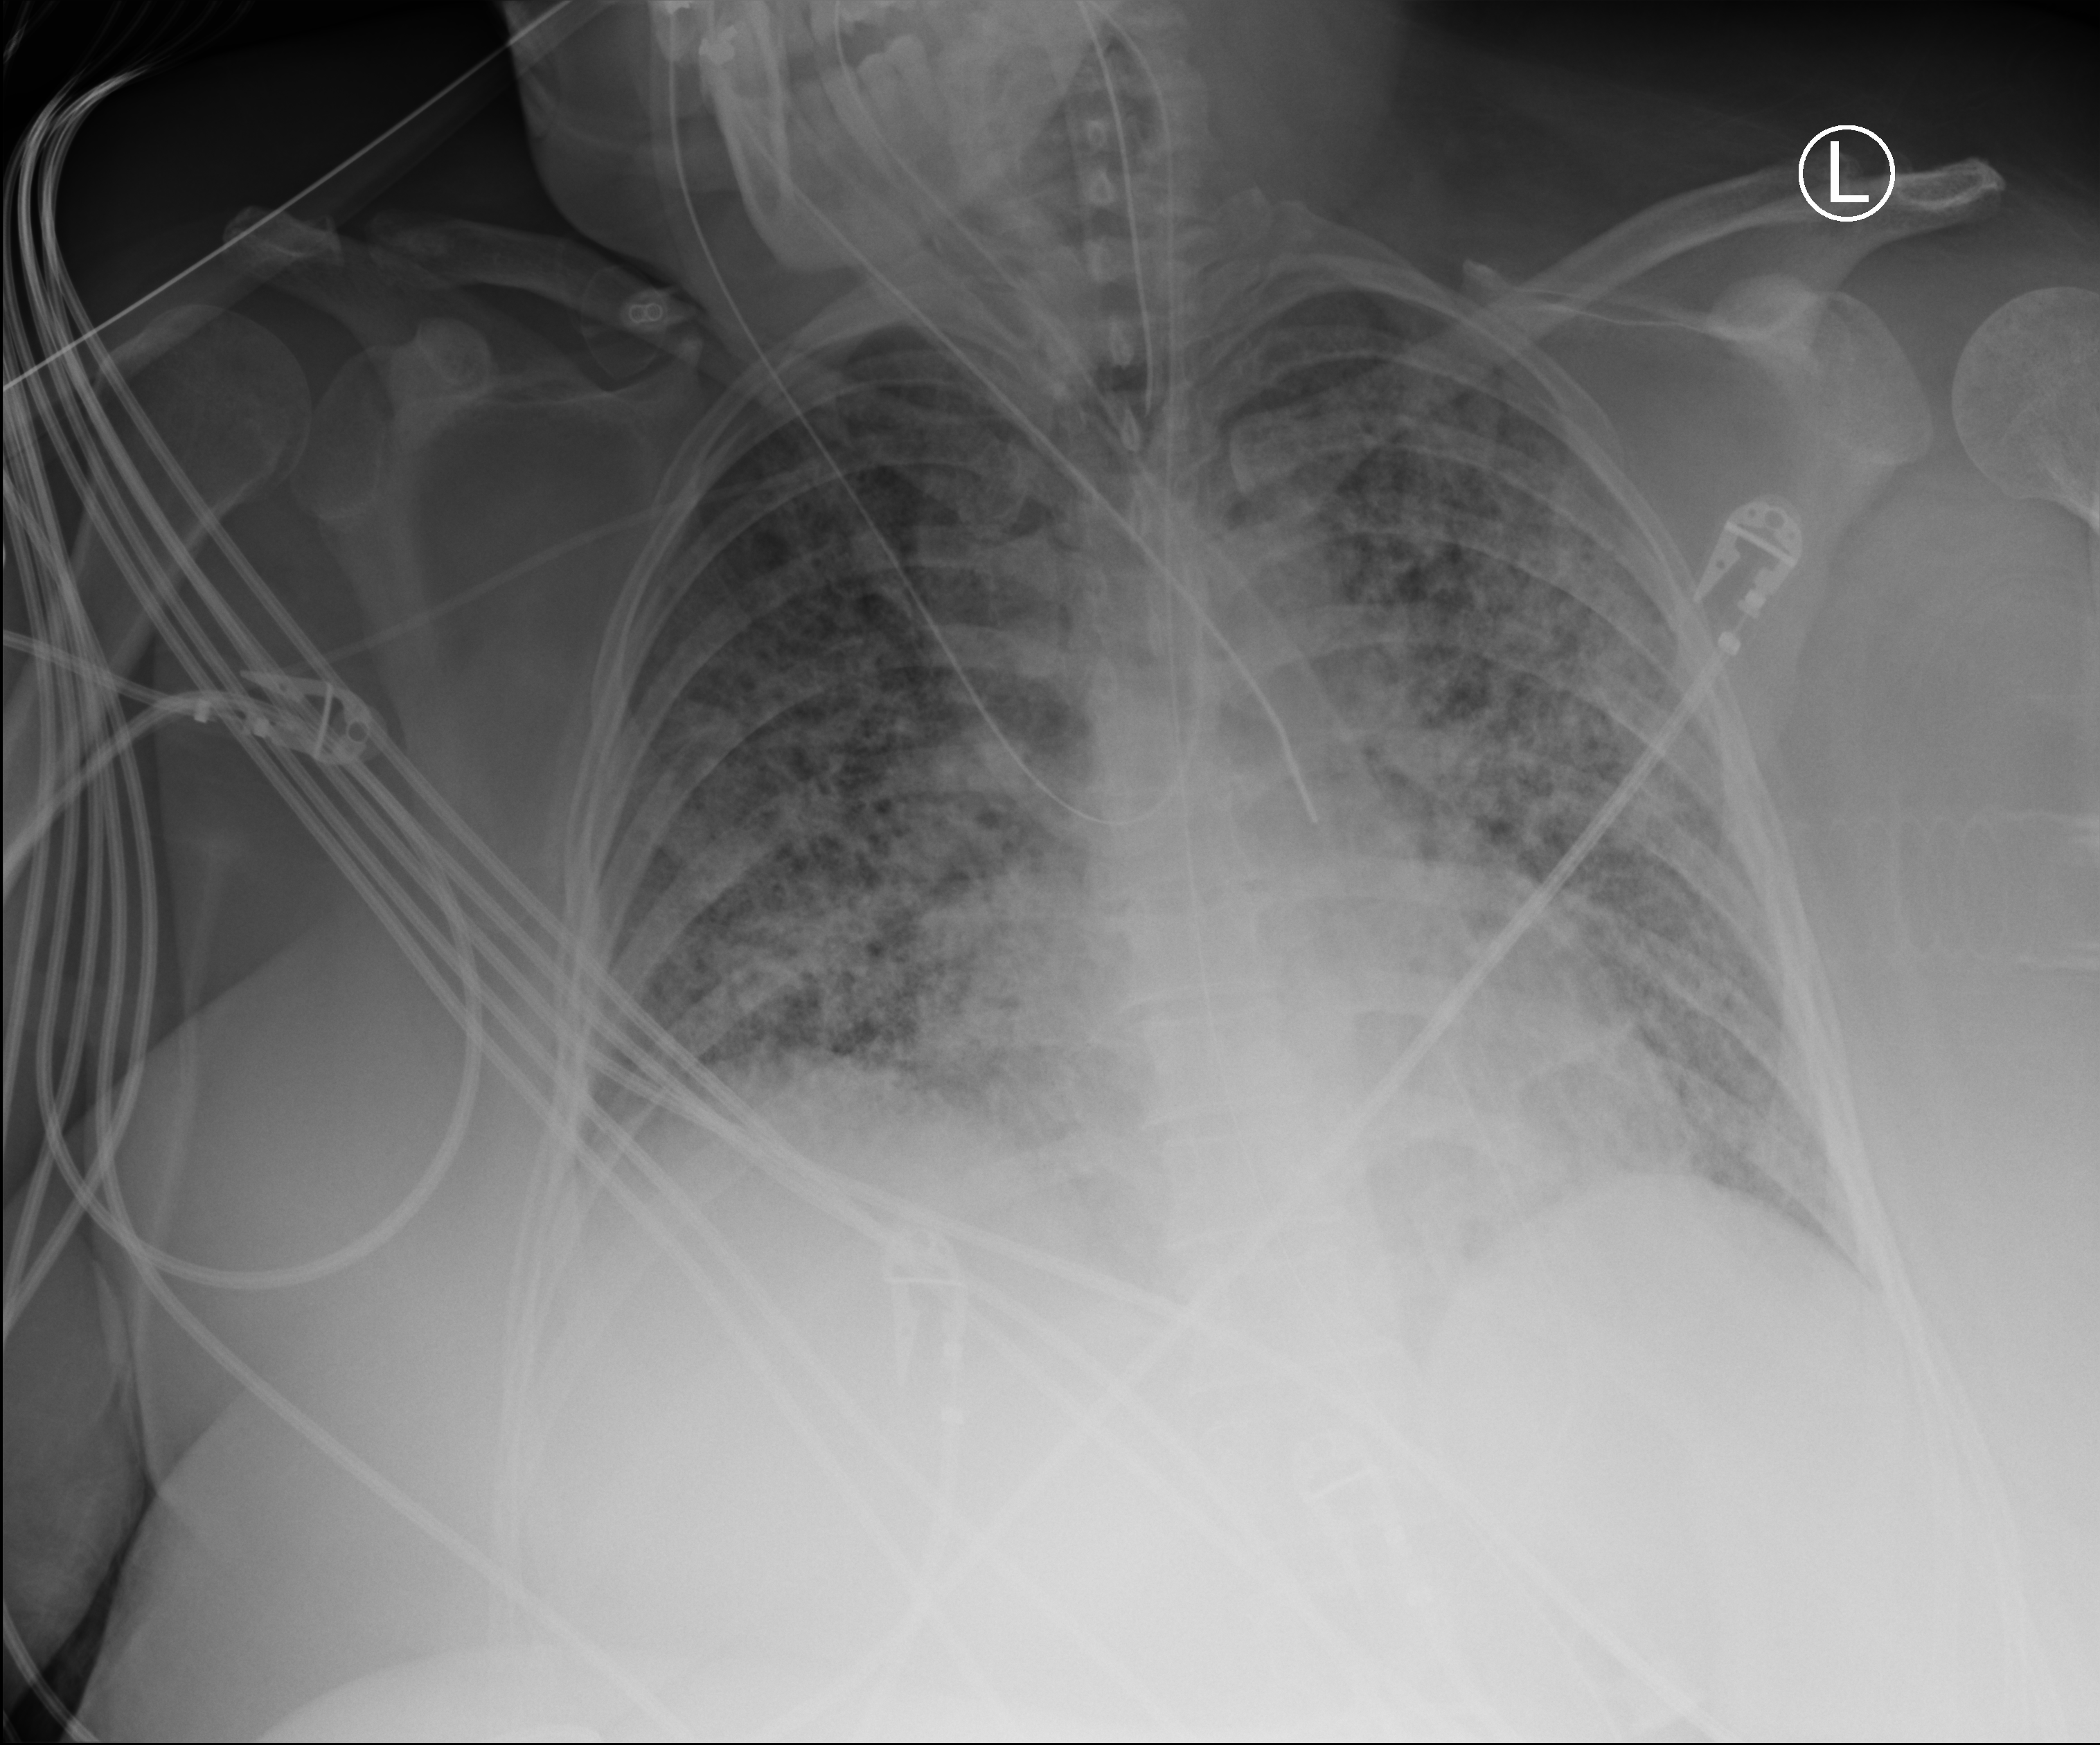
Portable chest radiograph; anteroposterior (AP) projection. Female patient hospitalised with COVID-19, age 18–59 years.
Hospital-stay facts (about this admission, not read from this image; timing relative to this image not recorded):
- mechanically ventilated during this hospital stay: yes
- admitted to intensive care during this hospital stay: yes